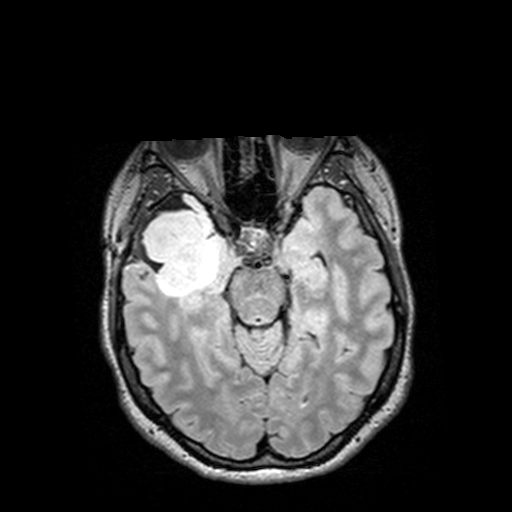
Brain MRI from a brain-tumour surgery series, one axial slice; slice 90 of 144 in the series (ordered by position); T2 FLAIR; 1 mm slice thickness; 512 × 512 image matrix. Case-level facts recorded for this patient, not image findings: histopathology: Astrocytoma; WHO grade: 3; IDH mutation: yes.
Annotated regions visible in this slice (manually delineated by an expert):
- tumour: bounding box [x1, y1, x2, y2] px = [132, 193, 224, 308]